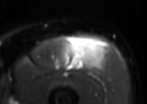
MRI of an extremity soft-tissue mass, one axial slice; position 40 of 85 along the scan axis; T2-weighted fat-saturated; MR volume resampled by the dataset authors to the PET/CT grid (not the native acquisition matrix); 3.27 mm slice thickness; 147 × 104 image matrix, field of view 144 × 102 mm. Male patient. From the clinical record (not read from this slice): histological type: extraskeletal osteosarcoma; grade: high; site of the primary tumour: thigh.
Annotated regions visible in this slice (expert contour drawn on MRI and transferred to this co-registered scan by the dataset authors):
- gross tumour volume (mass): bounding box <62,40,98,70> (left, top, right, bottom; pixels)